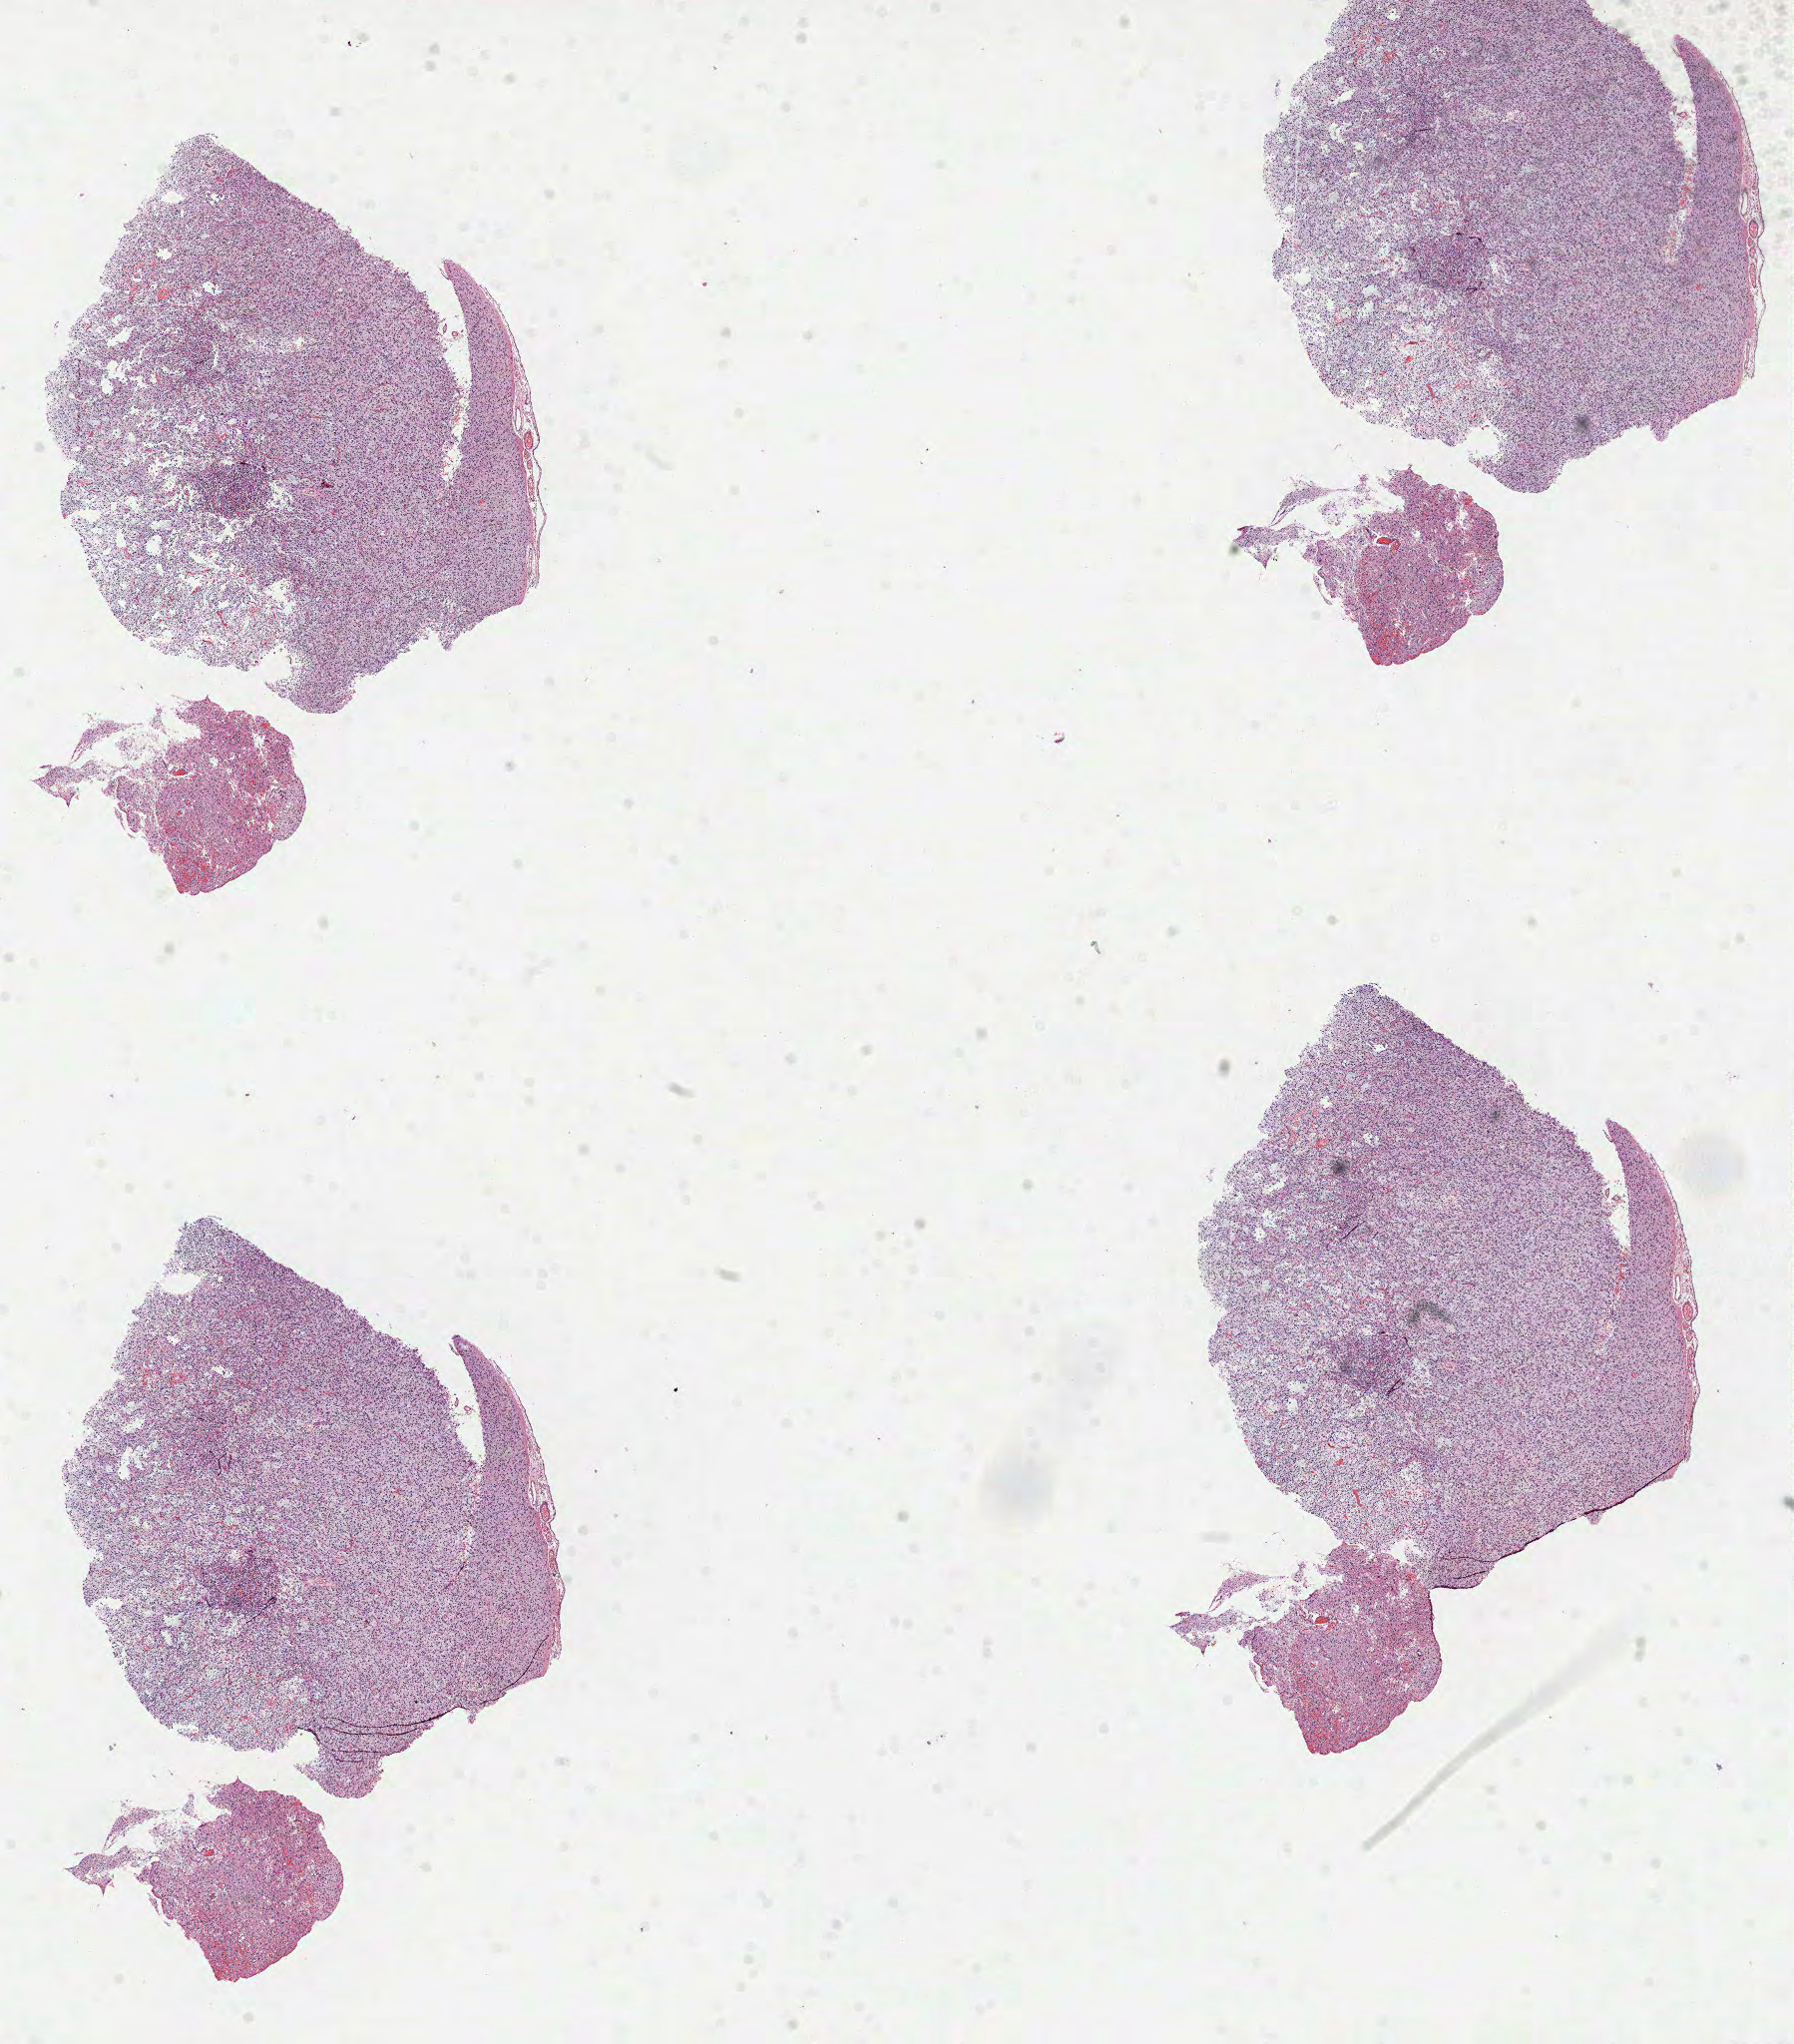
Digitized H&E-stained tissue section (whole slide) — shown as a low-resolution overview of the whole scanned area (about 14.5 x 16.5 mm), formalin-fixed paraffin-embedded (FFPE) diagnostic section, sample: primary tumour, brain. Female, age 37 years at initial diagnosis. Histologic grade: G2 (moderately differentiated).
• diagnosis: Mixed glioma